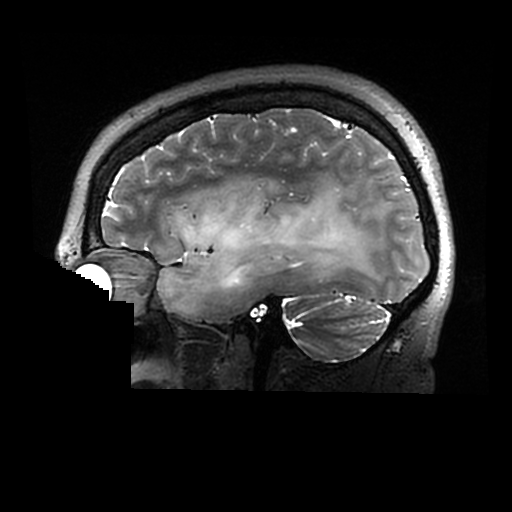
Brain MRI from a brain-tumour surgery series, one sagittal slice; 0.6 mm slice thickness; 512 × 512 image matrix, field of view 240 × 240 mm. Case-level facts recorded for this patient, not image findings: histopathology: Astrocytoma; WHO grade: 2; IDH mutation: yes.
Outlined on this slice (expert manual segmentation):
- tumour: box from (x=157, y=182) to (x=382, y=314) px